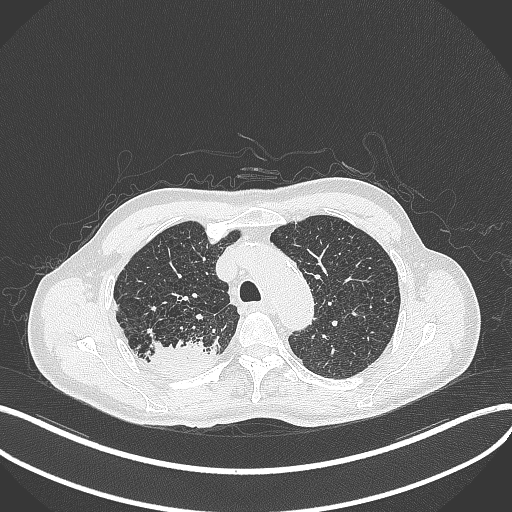
Chest CT, one axial slice. Position 338 of 428 along the scan axis. Reconstruction kernel B70f. 120 kVp. Lung window (W 1500 / L -600 HU). 1 mm slice thickness. 512 × 512 image matrix, field of view 400 × 400 mm. Male patient, age 79 years. Case-level facts recorded for this patient, not image findings: clinical TNM (as recorded): T3 N0 M0.
Annotated regions visible in this slice (rectangle marked by the reading radiologist):
- lung tumour (recorded histology: adenocarcinoma): bounding box [x1, y1, x2, y2] px = [148, 339, 221, 376]